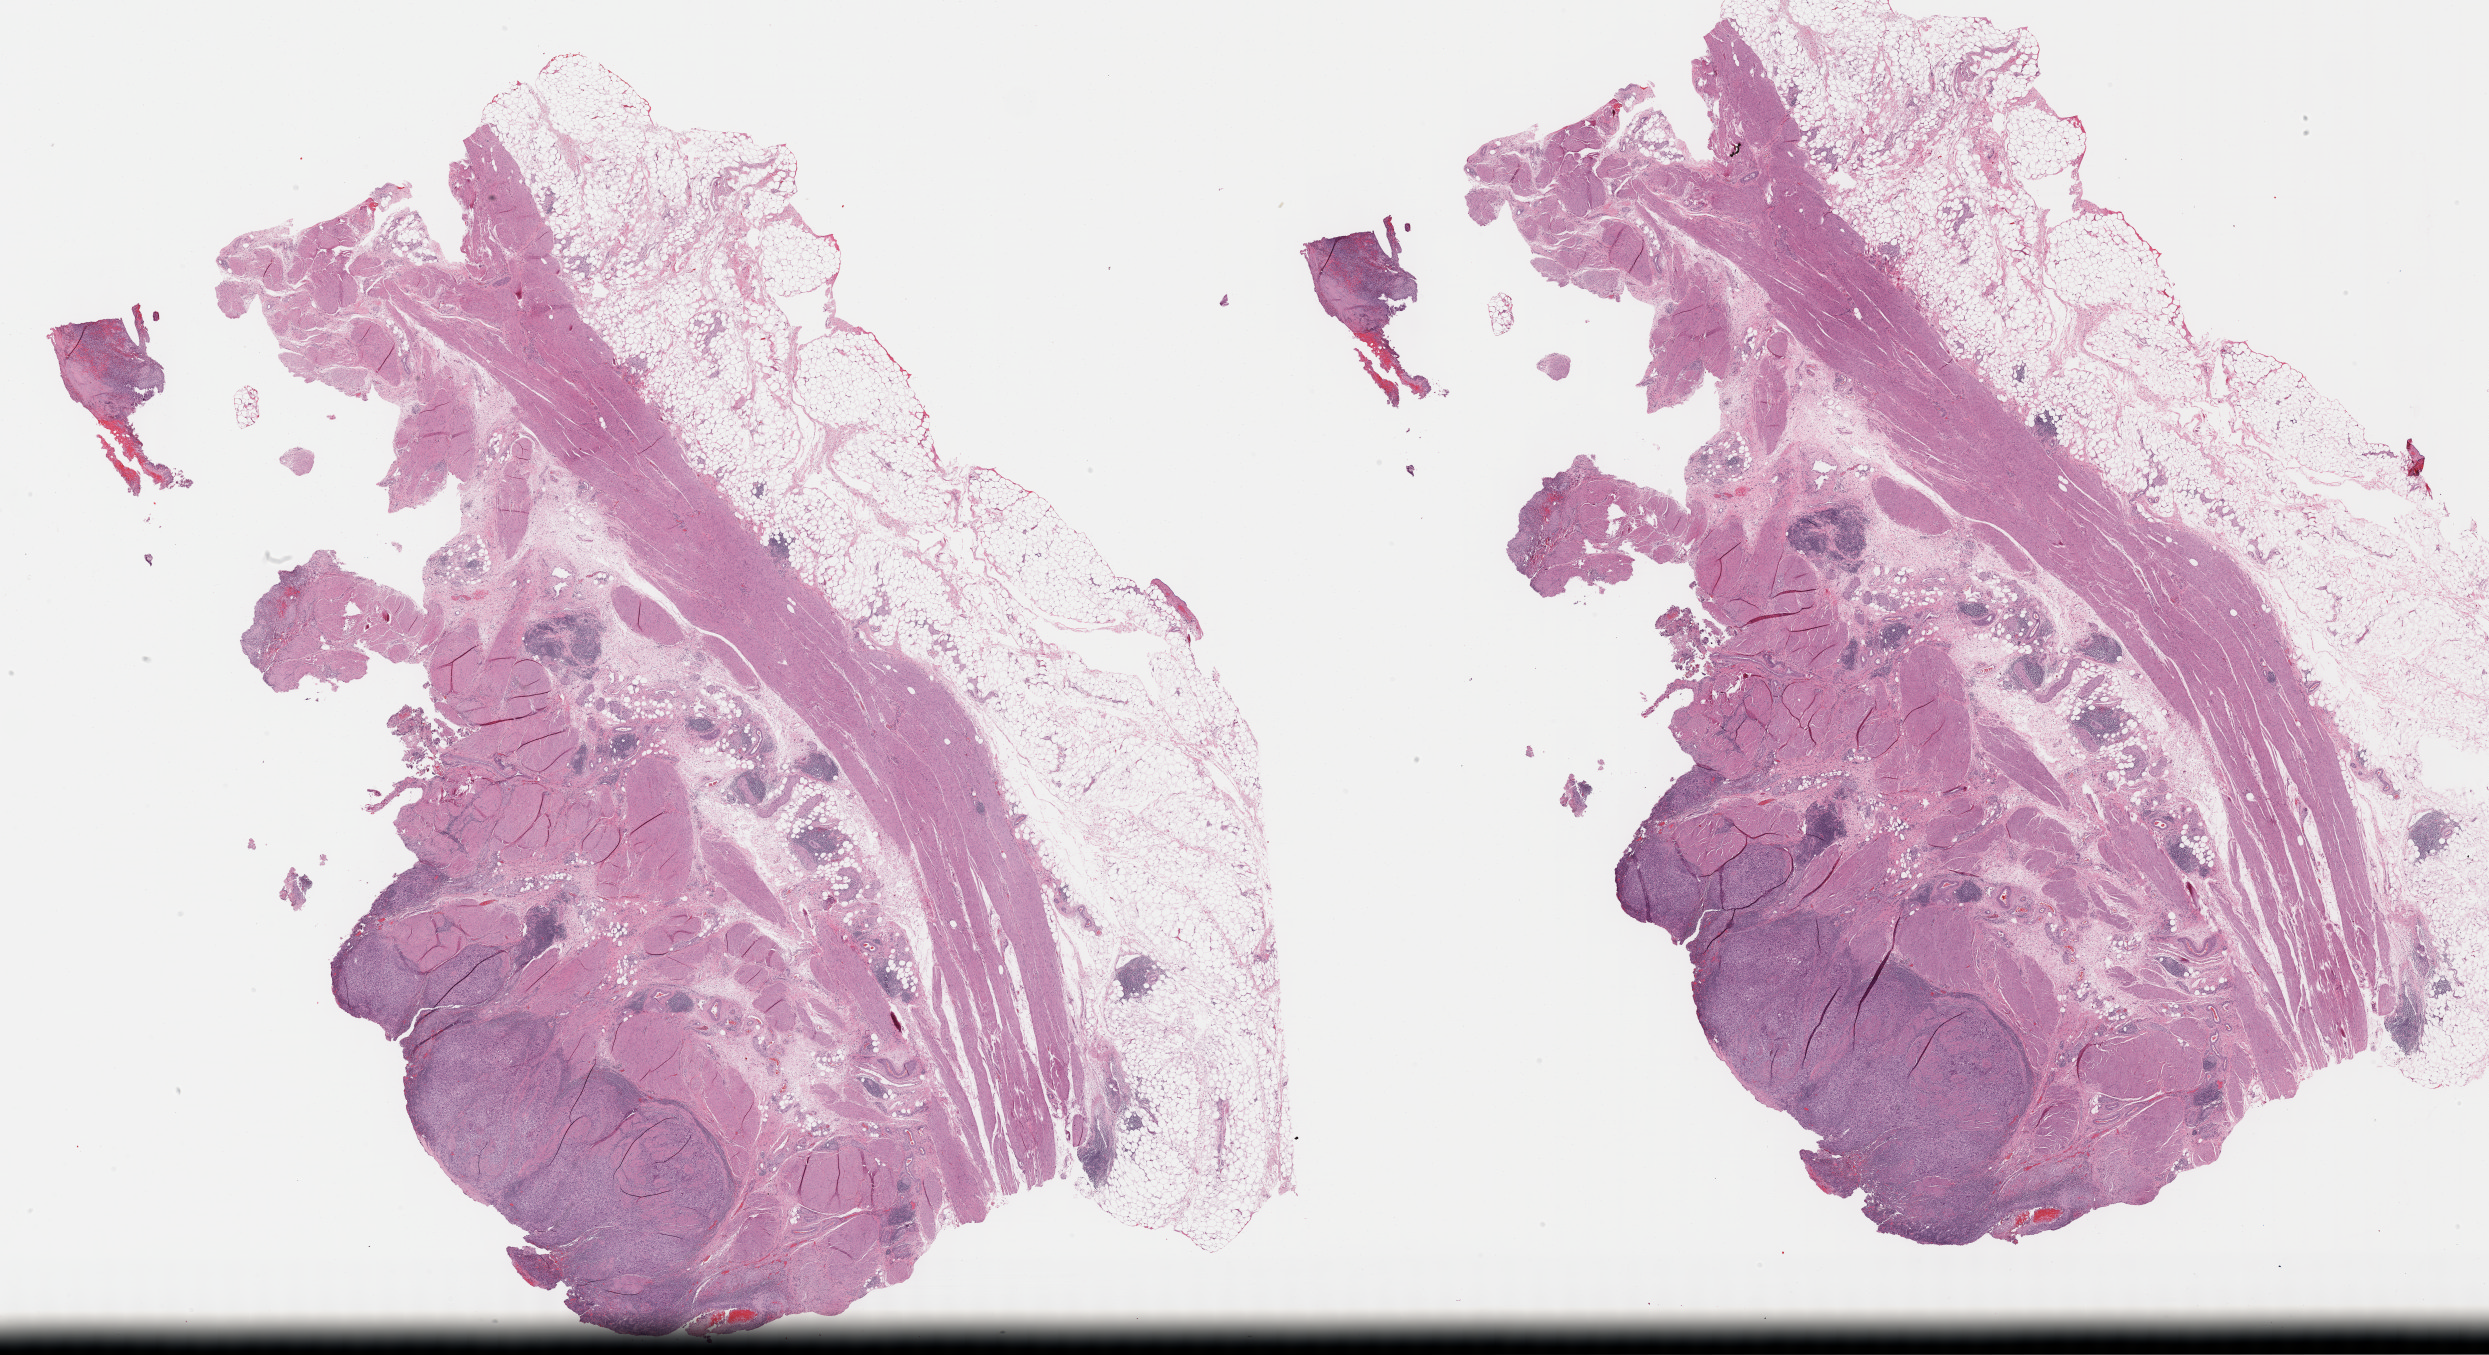
H&E-stained whole-slide image, low-resolution overview of the scanned area, about 40.3 x 21.9 mm (from a 40x scan). Formalin-fixed paraffin-embedded (FFPE) diagnostic section. Bladder, primary tumour sample. Patient: male, age at initial diagnosis 58 years. Histologic grade: high grade.
• AJCC pathologic stage: II (6th edition)
• TNM: T2b N0 M0
• histologic diagnosis: Transitional cell carcinoma (posterior wall of bladder)